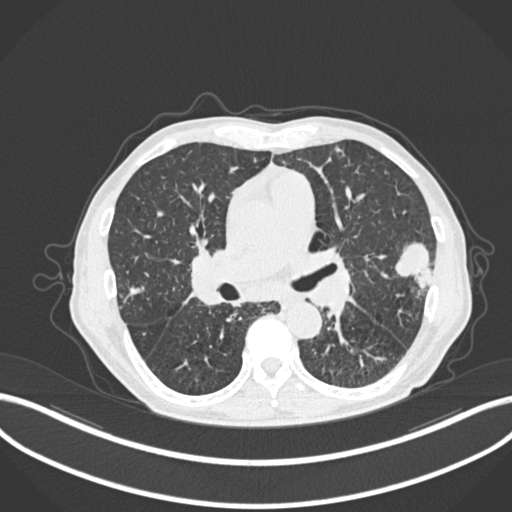
Chest CT, one axial slice. Slice 129 of 287 in the series (ordered by position). Reconstruction kernel B30f. 120 kVp. Lung window (W 1500 / L -600 HU). 512 × 512 image matrix, field of view 400 × 400 mm. Male patient, age 74 years. From the clinical record (not read from this slice): clinical TNM (as recorded): T2a N1 M0.
Annotated regions visible in this slice (bounding box drawn by a radiologist):
- lung tumour (recorded histology: adenocarcinoma): bounding box [x1, y1, x2, y2] px = [396, 238, 433, 289]